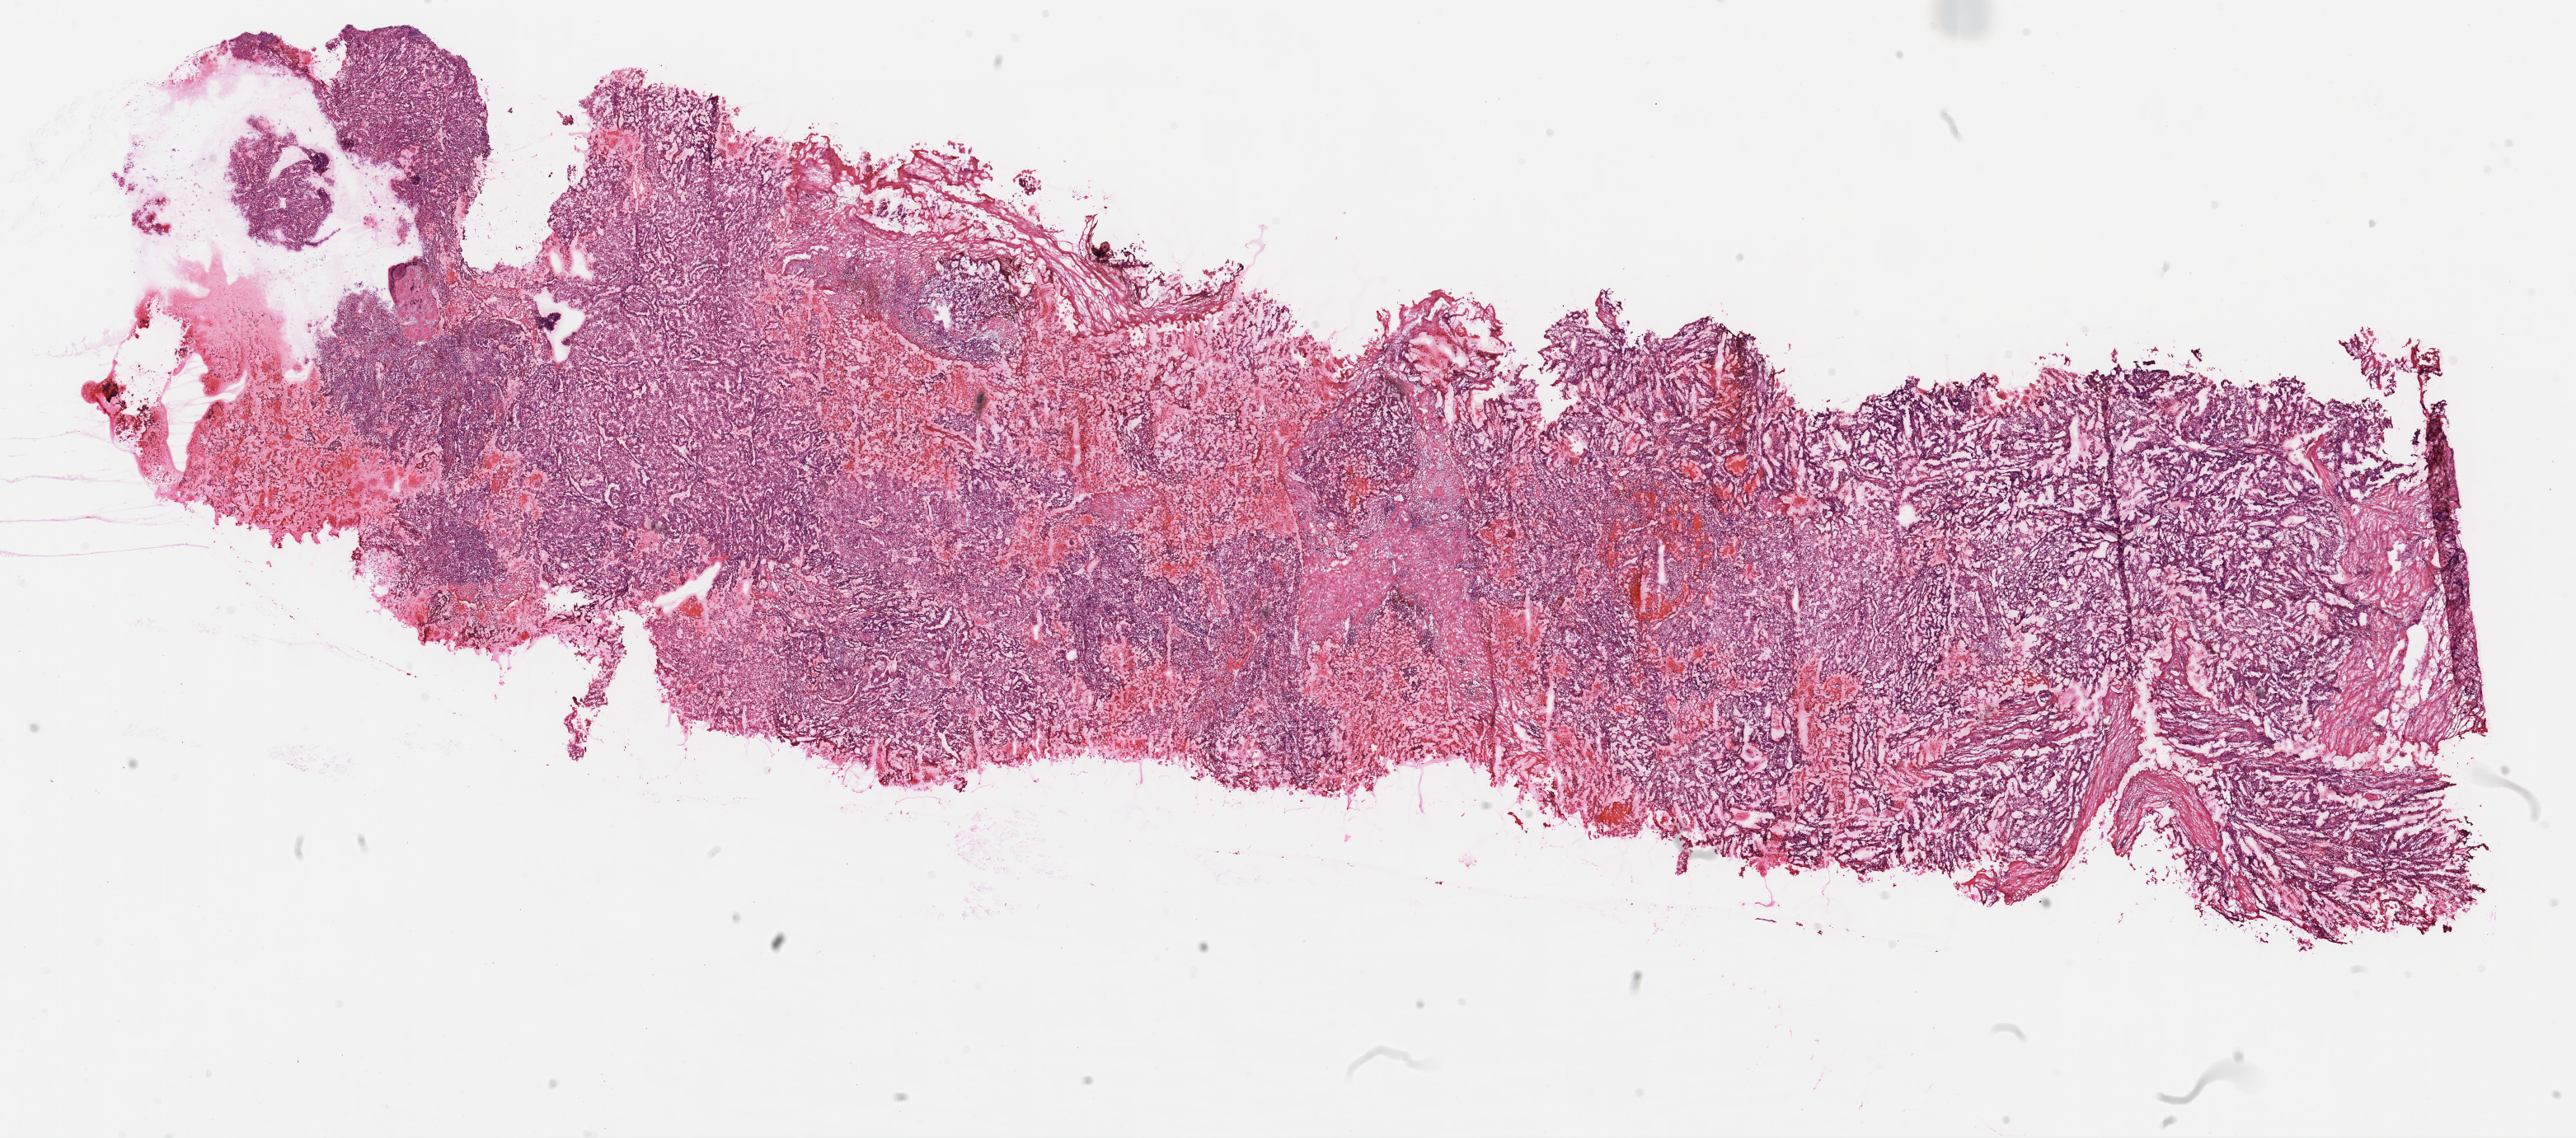
Digitized H&E tissue section (whole slide), whole scanned area (about 25.1 x 11.1 mm, from a 20x scan) shown as a low-resolution overview; frozen section from the top of the tissue portion; kidney, primary tumour sample. Male, age 51 years at initial diagnosis. Histologic grade: G3 (poorly differentiated). Composition of this section per pathologist review: tumour cells 80%, tumour nuclei 80%, normal cells 0%, stromal cells 20%, necrosis 0%.
* laterality: right
* AJCC pathologic stage: III
* diagnosis: Clear cell adenocarcinoma, NOS